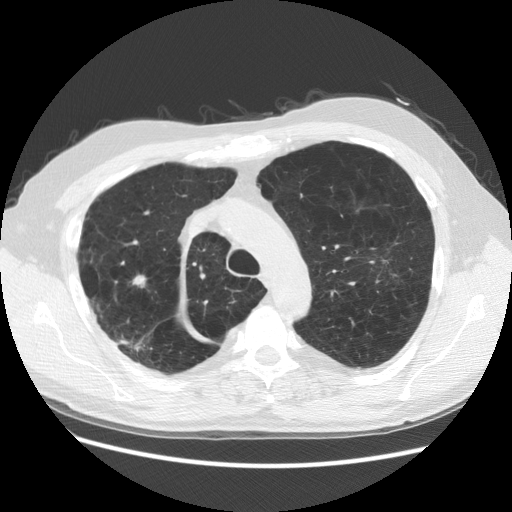
Low-dose screening chest CT, axial slice; third screening round (two years after baseline); lung window (W 1500 / L -600 HU); 2.5 mm slice thickness. Male participant, aged 58 years at enrolment. Former smoker at enrolment.
- Expert reader's lesion annotation, bounding box (x1, y1, x2, y2) in pixels: (112, 257, 161, 305).
- The screening reader recorded 3 non-calcified nodules or masses ≥4 mm on this exam; which of them this box marks is not recorded.
- Official screen result: positive, other.
- Later outcome: lung cancer diagnosed 88 days after this screen — squamous cell carcinoma, NOS, right upper lobe, moderately differentiated (G2), stage IB (AJCC 6th edition), 18 mm at pathology.